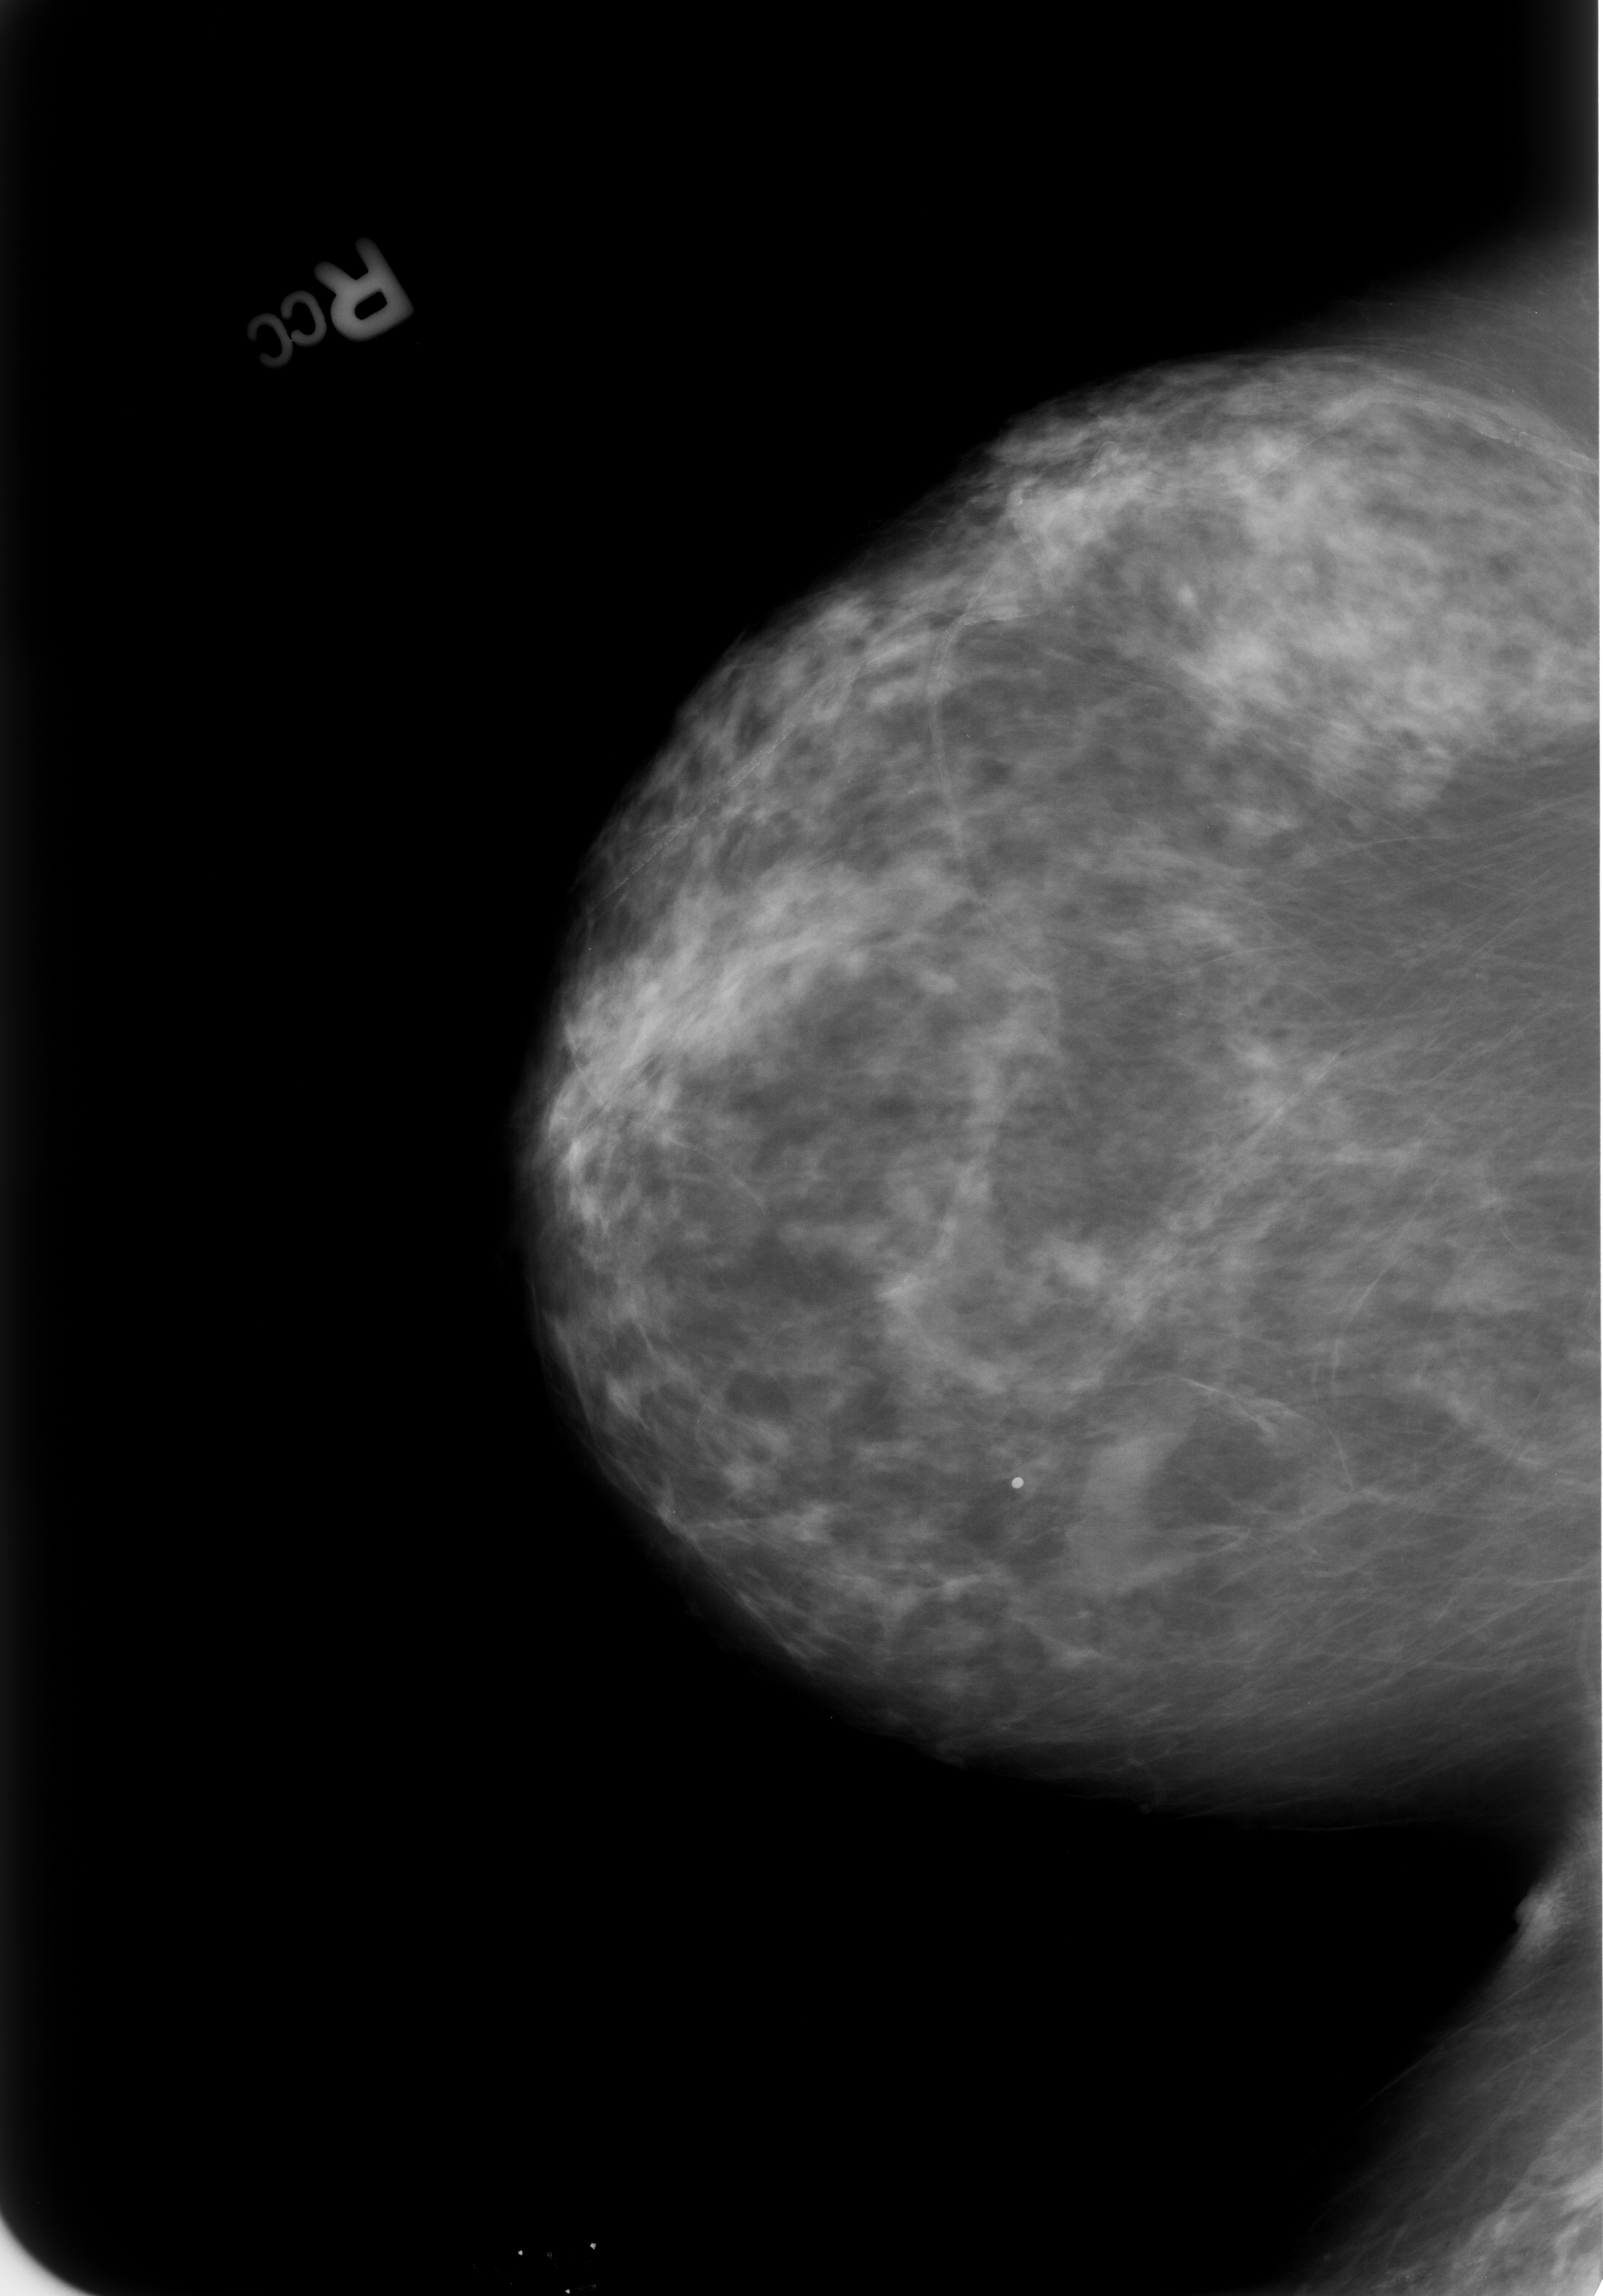
Digitized screen-film mammogram; right breast; craniocaudal (CC) view; breast composition: scattered fibroglandular densities (BI-RADS density category 2 of 4); 1603 × 2296 image matrix.
Expert-marked regions of interest on this image (one box per marked abnormality):
- Finding 1 of 4: calcifications, morphology vascular; BI-RADS assessment category 2; benign; no additional work-up was recommended (outcome (as recorded, no biopsy): benign without callback): bounding box (x1, y1, x2, y2) in pixels: (560, 586, 953, 1160)
- Finding 2 of 4: calcifications, morphology vascular; BI-RADS assessment category 2; benign; no additional work-up was recommended (outcome (as recorded, no biopsy): benign without callback): (867, 372, 1594, 1316)
- Finding 3 of 4: calcifications, morphology lucent center; BI-RADS assessment category 2; subtlety rating 4 on a 1 (subtle) to 5 (obvious) scale; benign; no additional work-up was recommended (outcome (as recorded, no biopsy): benign without callback): (974, 1454, 1044, 1529)
- Finding 4 of 4: calcifications, morphology vascular; BI-RADS assessment category 2; benign; no additional work-up was recommended (outcome (as recorded, no biopsy): benign without callback): (1466, 1143, 1601, 1280)